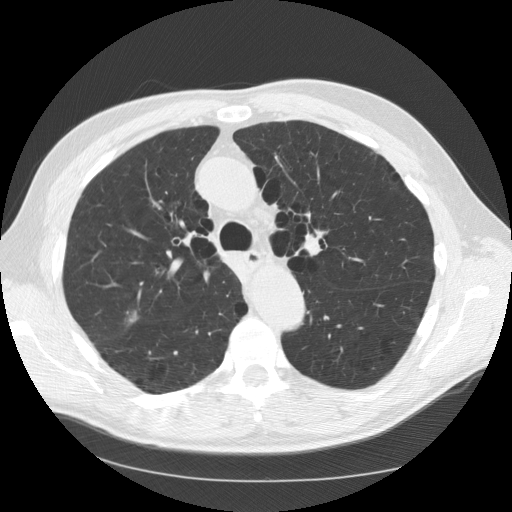
Low-dose screening chest CT, one axial slice; position 88 of 133 along the scan axis; reconstruction kernel STANDARD; lung window (W 1500 / L -600 HU); 2.5 mm slice thickness; 512 × 512 image matrix, field of view 377 × 377 mm.
Outlined on this slice (expert manual segmentation):
- lesion 1 (tumor, upper lobe of right lung): bounding box <129,311,137,323> (left, top, right, bottom; pixels)